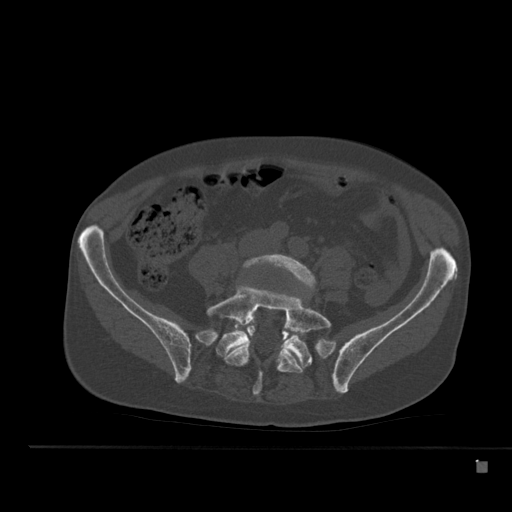
CT including the spine, one axial slice. Position 125 of 517 along the scan axis. Reconstruction kernel Br40s. 120 kVp. Bone window (W 1800 / L 400 HU). 1.5 mm slice thickness. 512 × 512 image matrix, field of view 408 × 408 mm. Patient: male, 70 years. Case-level facts recorded for this patient, not image findings: primary cancer: renal.
Annotated regions visible in this slice (semi-automatically segmented with operator editing):
- L4 vertebra: bounding box [x1, y1, x2, y2] px = [242, 254, 316, 327]
- L5 vertebra: [206, 285, 332, 396]